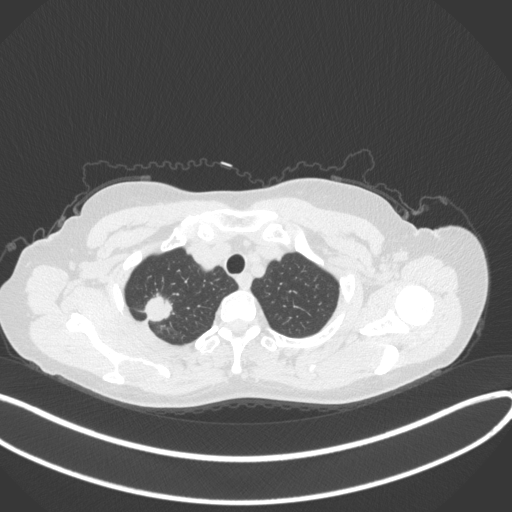
Chest CT, one axial slice. Position 317 of 342 along the scan axis. 120 kVp. Lung window (W 1500 / L -600 HU). 512 × 512 image matrix, field of view 400 × 400 mm. Female patient, age 50 years. Case-level facts recorded for this patient, not image findings: clinical TNM (as recorded): T1c N0 M0; histopathological grade: G2-3.
Structures marked on this image (rectangle marked by the reading radiologist):
- lung tumour (recorded histology: adenocarcinoma): box from (x=140, y=292) to (x=173, y=325) px